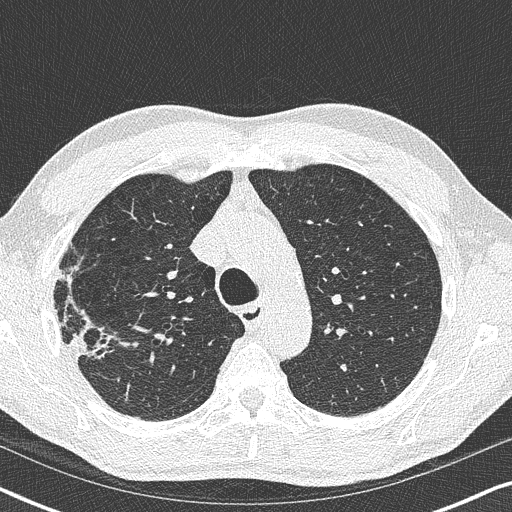
Low-dose screening chest CT, one axial slice; position 270 of 356 along the scan axis; 120 kVp; lung window (W 1500 / L -600 HU); 1 mm slice thickness; 512 × 512 image matrix, field of view 330 × 330 mm.
Structures marked on this image (expert manual segmentation):
- lesion 1 (tumor, upper lobe of right lung): bounding box (x1, y1, x2, y2) in pixels: (67, 312, 114, 361)